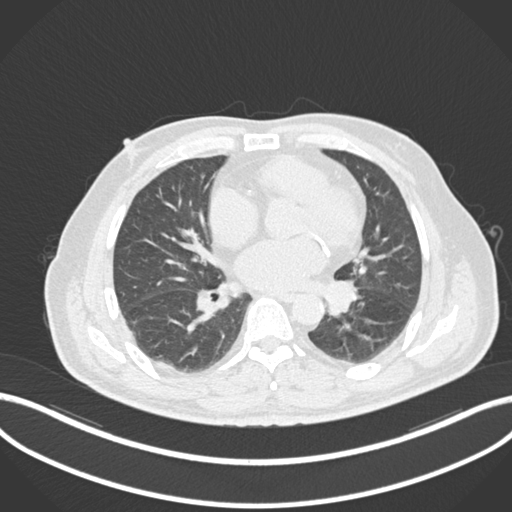
Chest CT, one axial slice; reconstruction kernel B30f; 120 kVp; lung window (W 1500 / L -600 HU); 1 mm slice thickness; 512 × 512 image matrix, field of view 400 × 400 mm. Patient: male, 71 years. Case-level facts recorded for this patient, not image findings: clinical TNM (as recorded): T1b N0 M0.
Outlined on this slice (rectangle marked by the reading radiologist):
- lung tumour (recorded histology: squamous cell carcinoma): bounding box (x1, y1, x2, y2) in pixels: (322, 276, 357, 319)